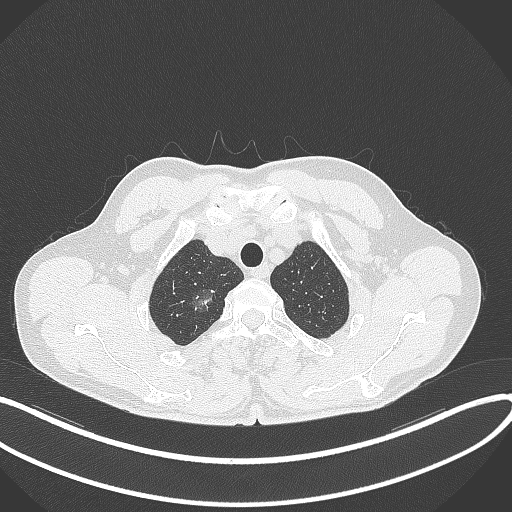
Chest CT, one axial slice; slice 337 of 407 in the series (ordered by position); 120 kVp; lung window (W 1500 / L -600 HU); 512 × 512 image matrix, field of view 400 × 400 mm. Patient: male, 58 years. From the clinical record (not read from this slice): clinical TNM (as recorded): T1c N0 M0.
Outlined on this slice (bounding box drawn by a radiologist):
- lung tumour (recorded histology: adenocarcinoma): bounding box (x1, y1, x2, y2) in pixels: (187, 283, 218, 315)